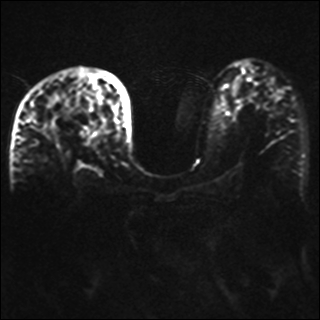
Breast MRI, one axial slice; slice 19 of 42 in the series (ordered by position); diffusion-weighted series; image 2 of 4 stored at this slice position (different b-values; order by instance number); 1.5 T; 4 mm slice thickness; 320 × 320 image matrix, field of view 330 × 330 mm. Female patient.
Structures marked on this image (outlined manually by an expert reader):
- tumour on diffusion-weighted imaging: bounding box <48,121,56,130> (left, top, right, bottom; pixels)